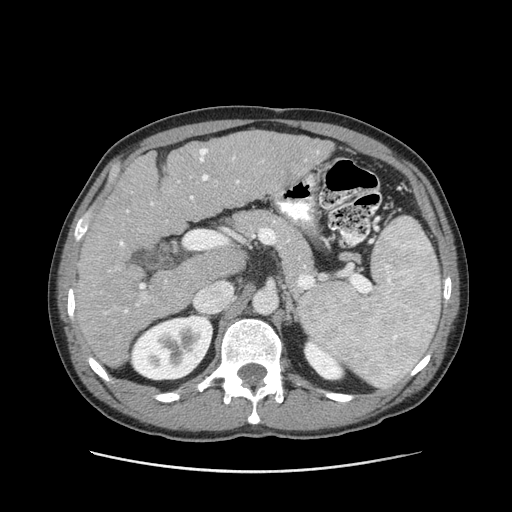
Contrast-enhanced abdominal CT (liver protocol), one axial slice; position 53 of 93 along the scan axis; reconstruction kernel STANDARD; 120 kVp; soft-tissue window (W 400 / L 40 HU); 2.5 mm slice thickness; 512 × 512 image matrix, field of view 380 × 380 mm. From the clinical record (not read from this slice): diagnosis: hepatocellular carcinoma (patient treated with transarterial chemoembolisation; whether this scan precedes or follows treatment is not stated here); TNM stage (as recorded): Stage-II; Child-Pugh class: A.
Annotated regions visible in this slice (semi-automatic segmentation, software-assisted and operator-edited):
- liver parenchyma outside the tumour (the mass and vessels are separate outlines, so this box may not span the whole liver): box from (x=74, y=130) to (x=332, y=368) px
- liver vessels: (x=104, y=148)–(x=264, y=314)